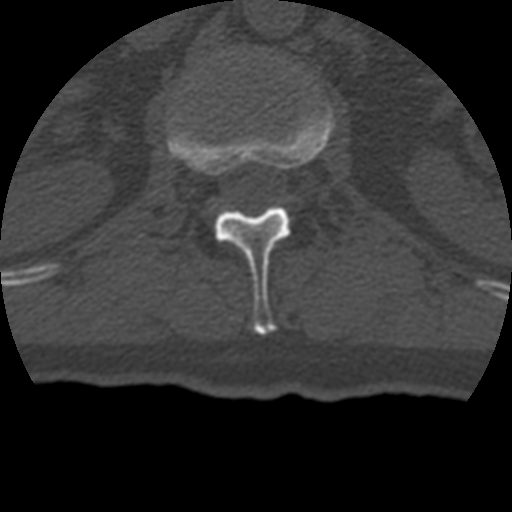
CT including the spine, one axial slice; slice 138 of 399 in the series (ordered by position); reconstruction kernel STANDARD; 120 kVp; bone window (W 1800 / L 400 HU); 512 × 512 image matrix, field of view 160 × 160 mm. Patient age 69 years. Case-level facts recorded for this patient, not image findings: primary cancer: prostate.
Outlined on this slice (semi-automatically segmented with operator editing):
- L1 vertebra: bounding box [x1, y1, x2, y2] px = [167, 101, 335, 335]